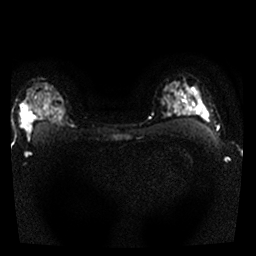
Breast MRI, one axial slice. Slice 21 of 25 in the series (ordered by position). Diffusion-weighted series; image 2 of 4 stored at this slice position (different b-values; order by instance number). 1.5 T. 4 mm slice thickness. 256 × 256 image matrix. Female patient.
Outlined on this slice (manually delineated by an expert):
- tumour on diffusion-weighted imaging: box from (x=22, y=105) to (x=48, y=130) px